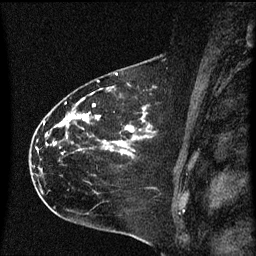
Breast MRI (dynamic contrast-enhanced), one sagittal slice; position 40 of 60 along the scan axis; dynamic contrast-enhanced series, image 2 of 3 at this slice position (ordered by acquisition); 1.5 T; TE 4.2 ms, TR 8.4 ms; 2 mm slice thickness; 256 × 256 image matrix. Patient: female, 35 years. Case-level facts recorded for this patient, not image findings: setting: breast cancer imaged before/during neoadjuvant chemotherapy; receptor status: HER2-positive.
Structures marked on this image (semi-automatic segmentation, software-assisted and operator-edited):
- analysis volume of interest (the breast-tissue region the enhancement analysis was run in; not a lesion): box from (x=31, y=68) to (x=173, y=173) px
- tumour enhancement mask (voxels above the 70 % enhancement threshold inside the analysis volume of interest): (x=49, y=98)–(x=150, y=155)